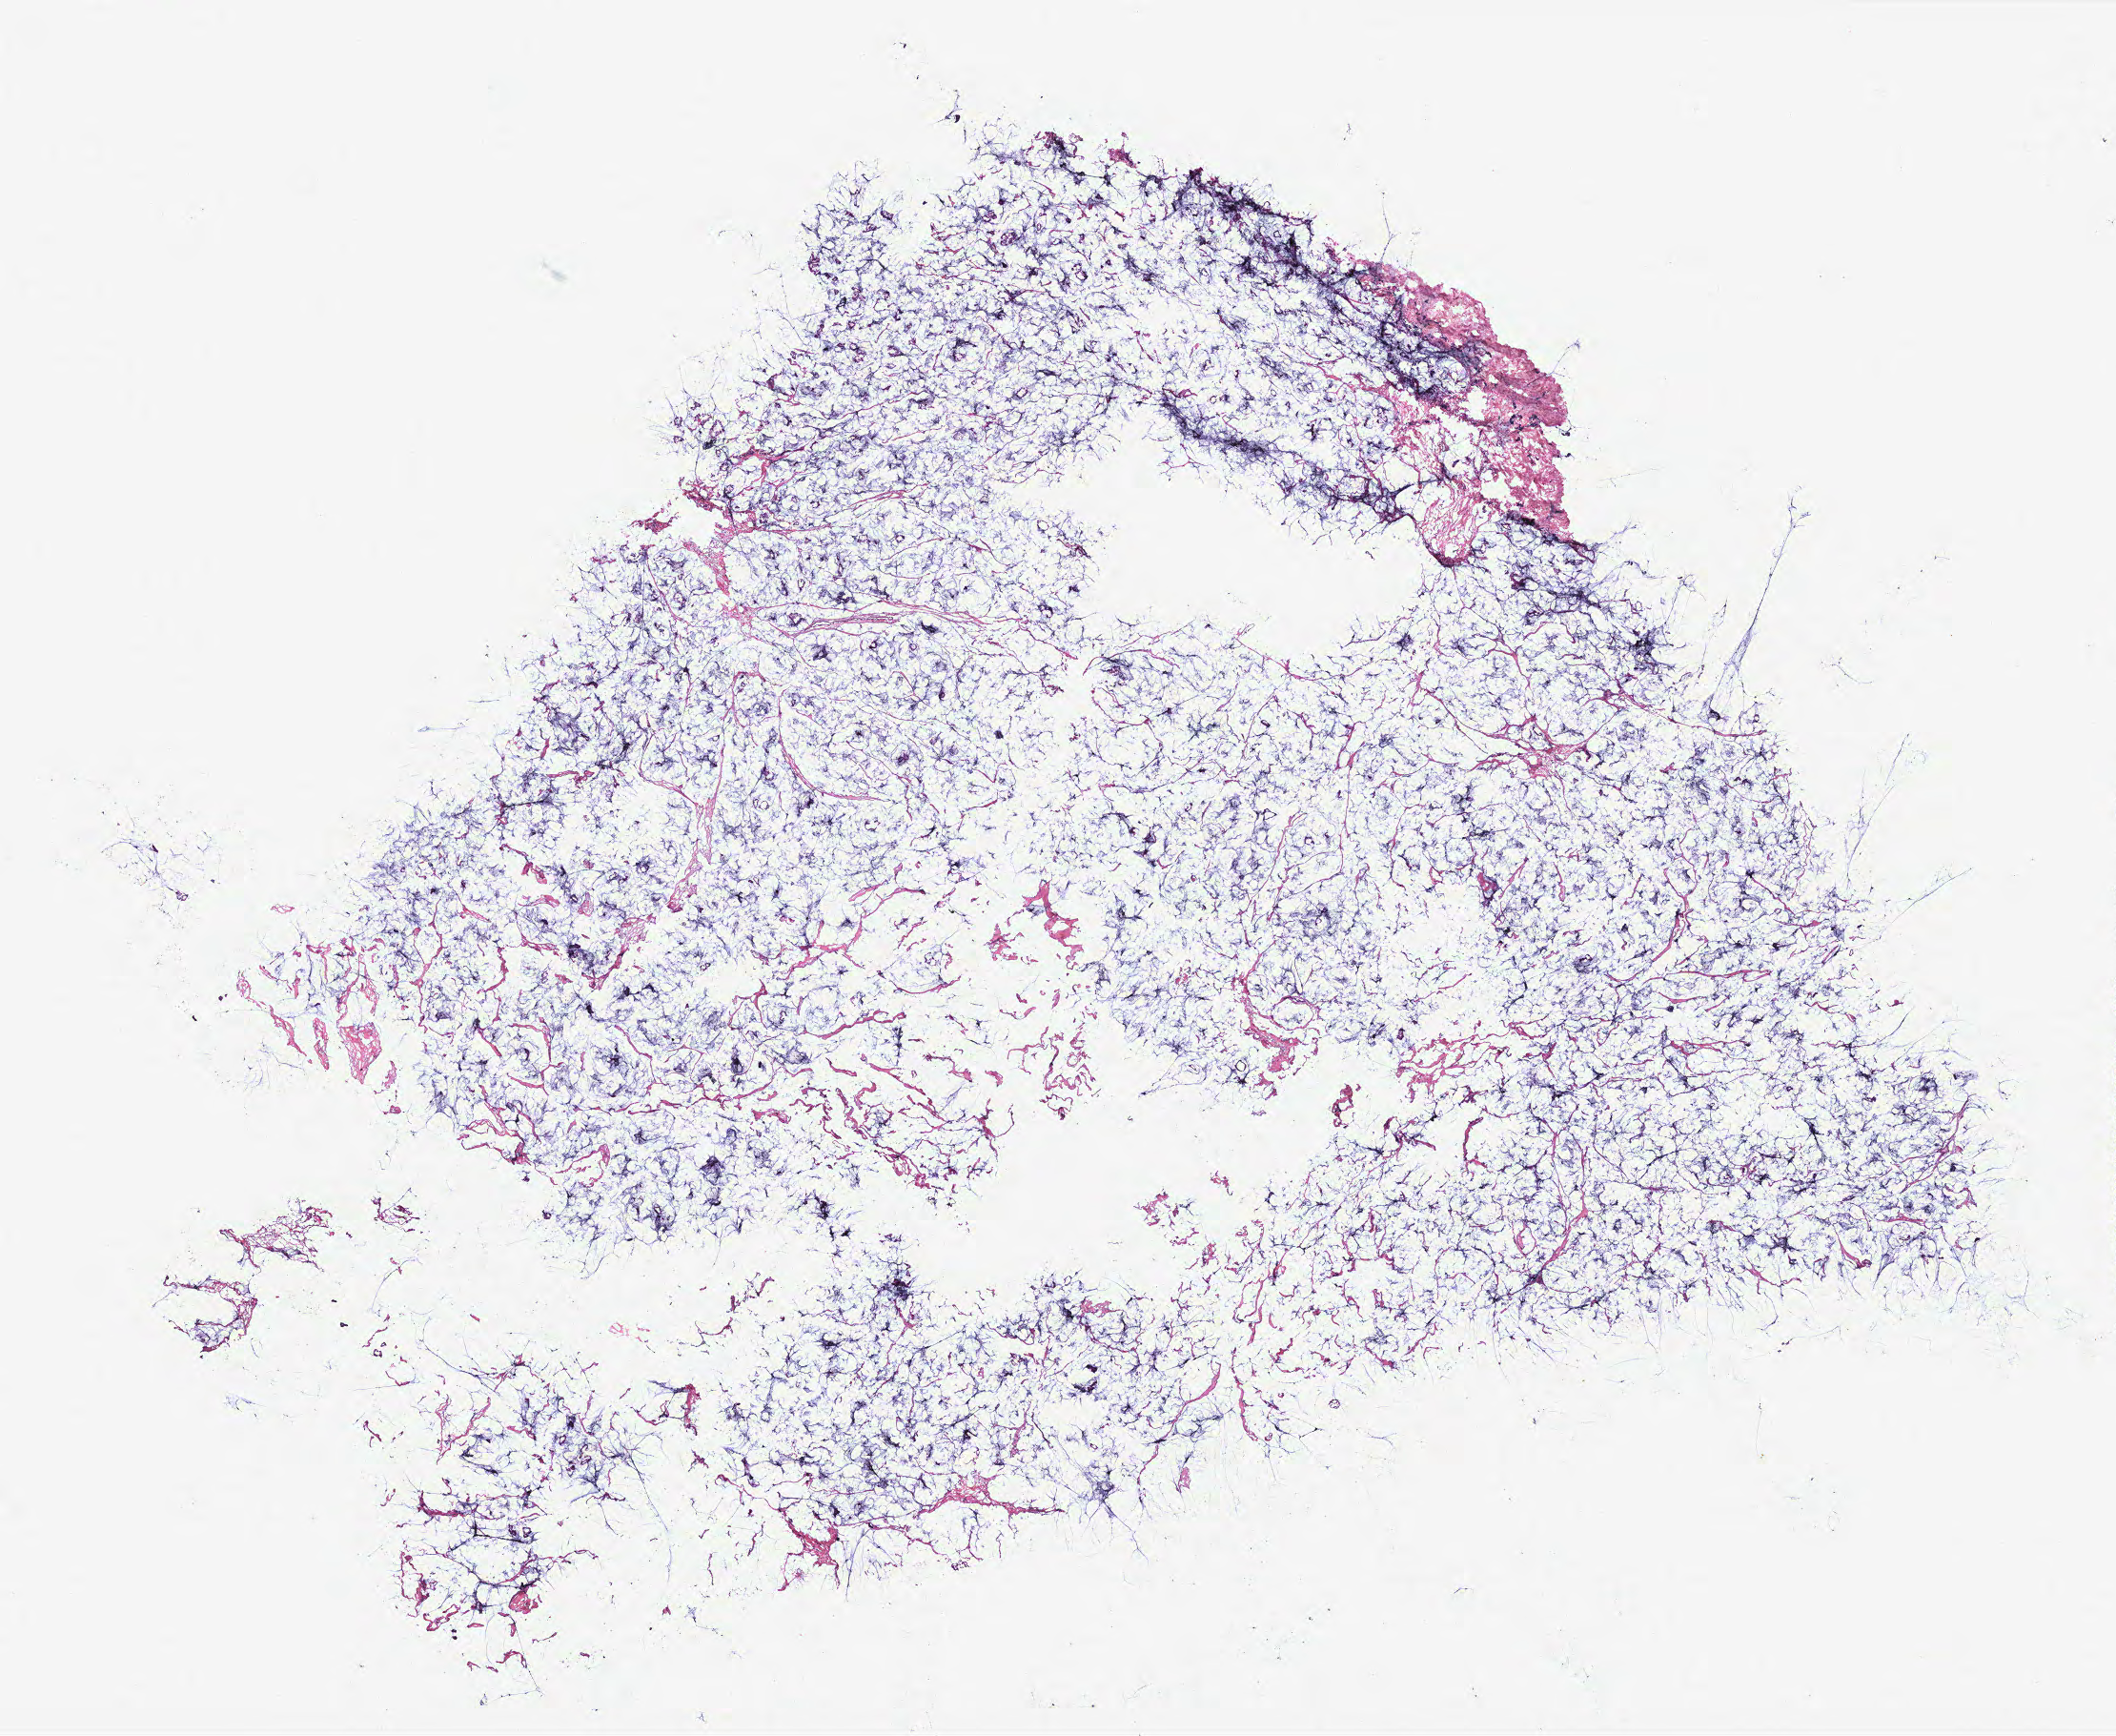
Digitized H&E-stained tissue section (whole slide), low-resolution overview of the scanned area, about 17.8 x 14.6 mm, tumour tissue sample, breast. Patient: female, age 54 years.
* AJCC pathologic stage: IIA
* histologic diagnosis: Mucinous carcinoma